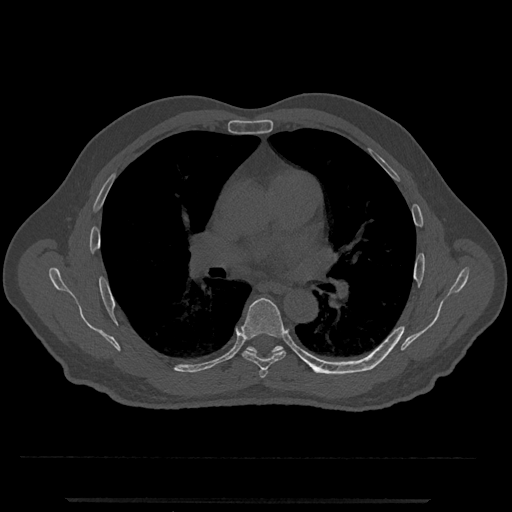
CT including the spine, one axial slice. Slice 726 of 797 in the series (ordered by position). Reconstruction kernel Br40s/3. Bone window (W 1800 / L 400 HU). 0.5 mm slice thickness. 512 × 512 image matrix. Patient: male, 63 years. From the clinical record (not read from this slice): primary cancer: prostate.
Outlined on this slice (semi-automatic segmentation, software-assisted and operator-edited):
- T5 vertebra: bounding box <259,369,268,378> (left, top, right, bottom; pixels)
- T6 vertebra: <241,298,286,371>
- T7 vertebra: <246,346,329,375>